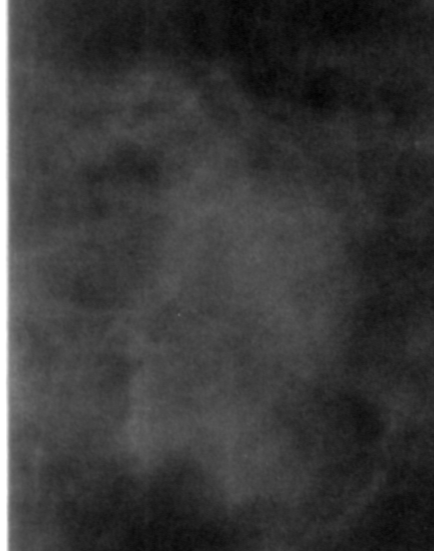
Cropped region of a digitized screen-film mammogram centred on a radiologist-marked abnormality; right breast; CC view.
- Mass, shape irregular, margins ill defined; BI-RADS assessment category 4; subtlety rating 2 on a 1 (subtle) to 5 (obvious) scale; pathology result (as recorded, not read from the image): benign.